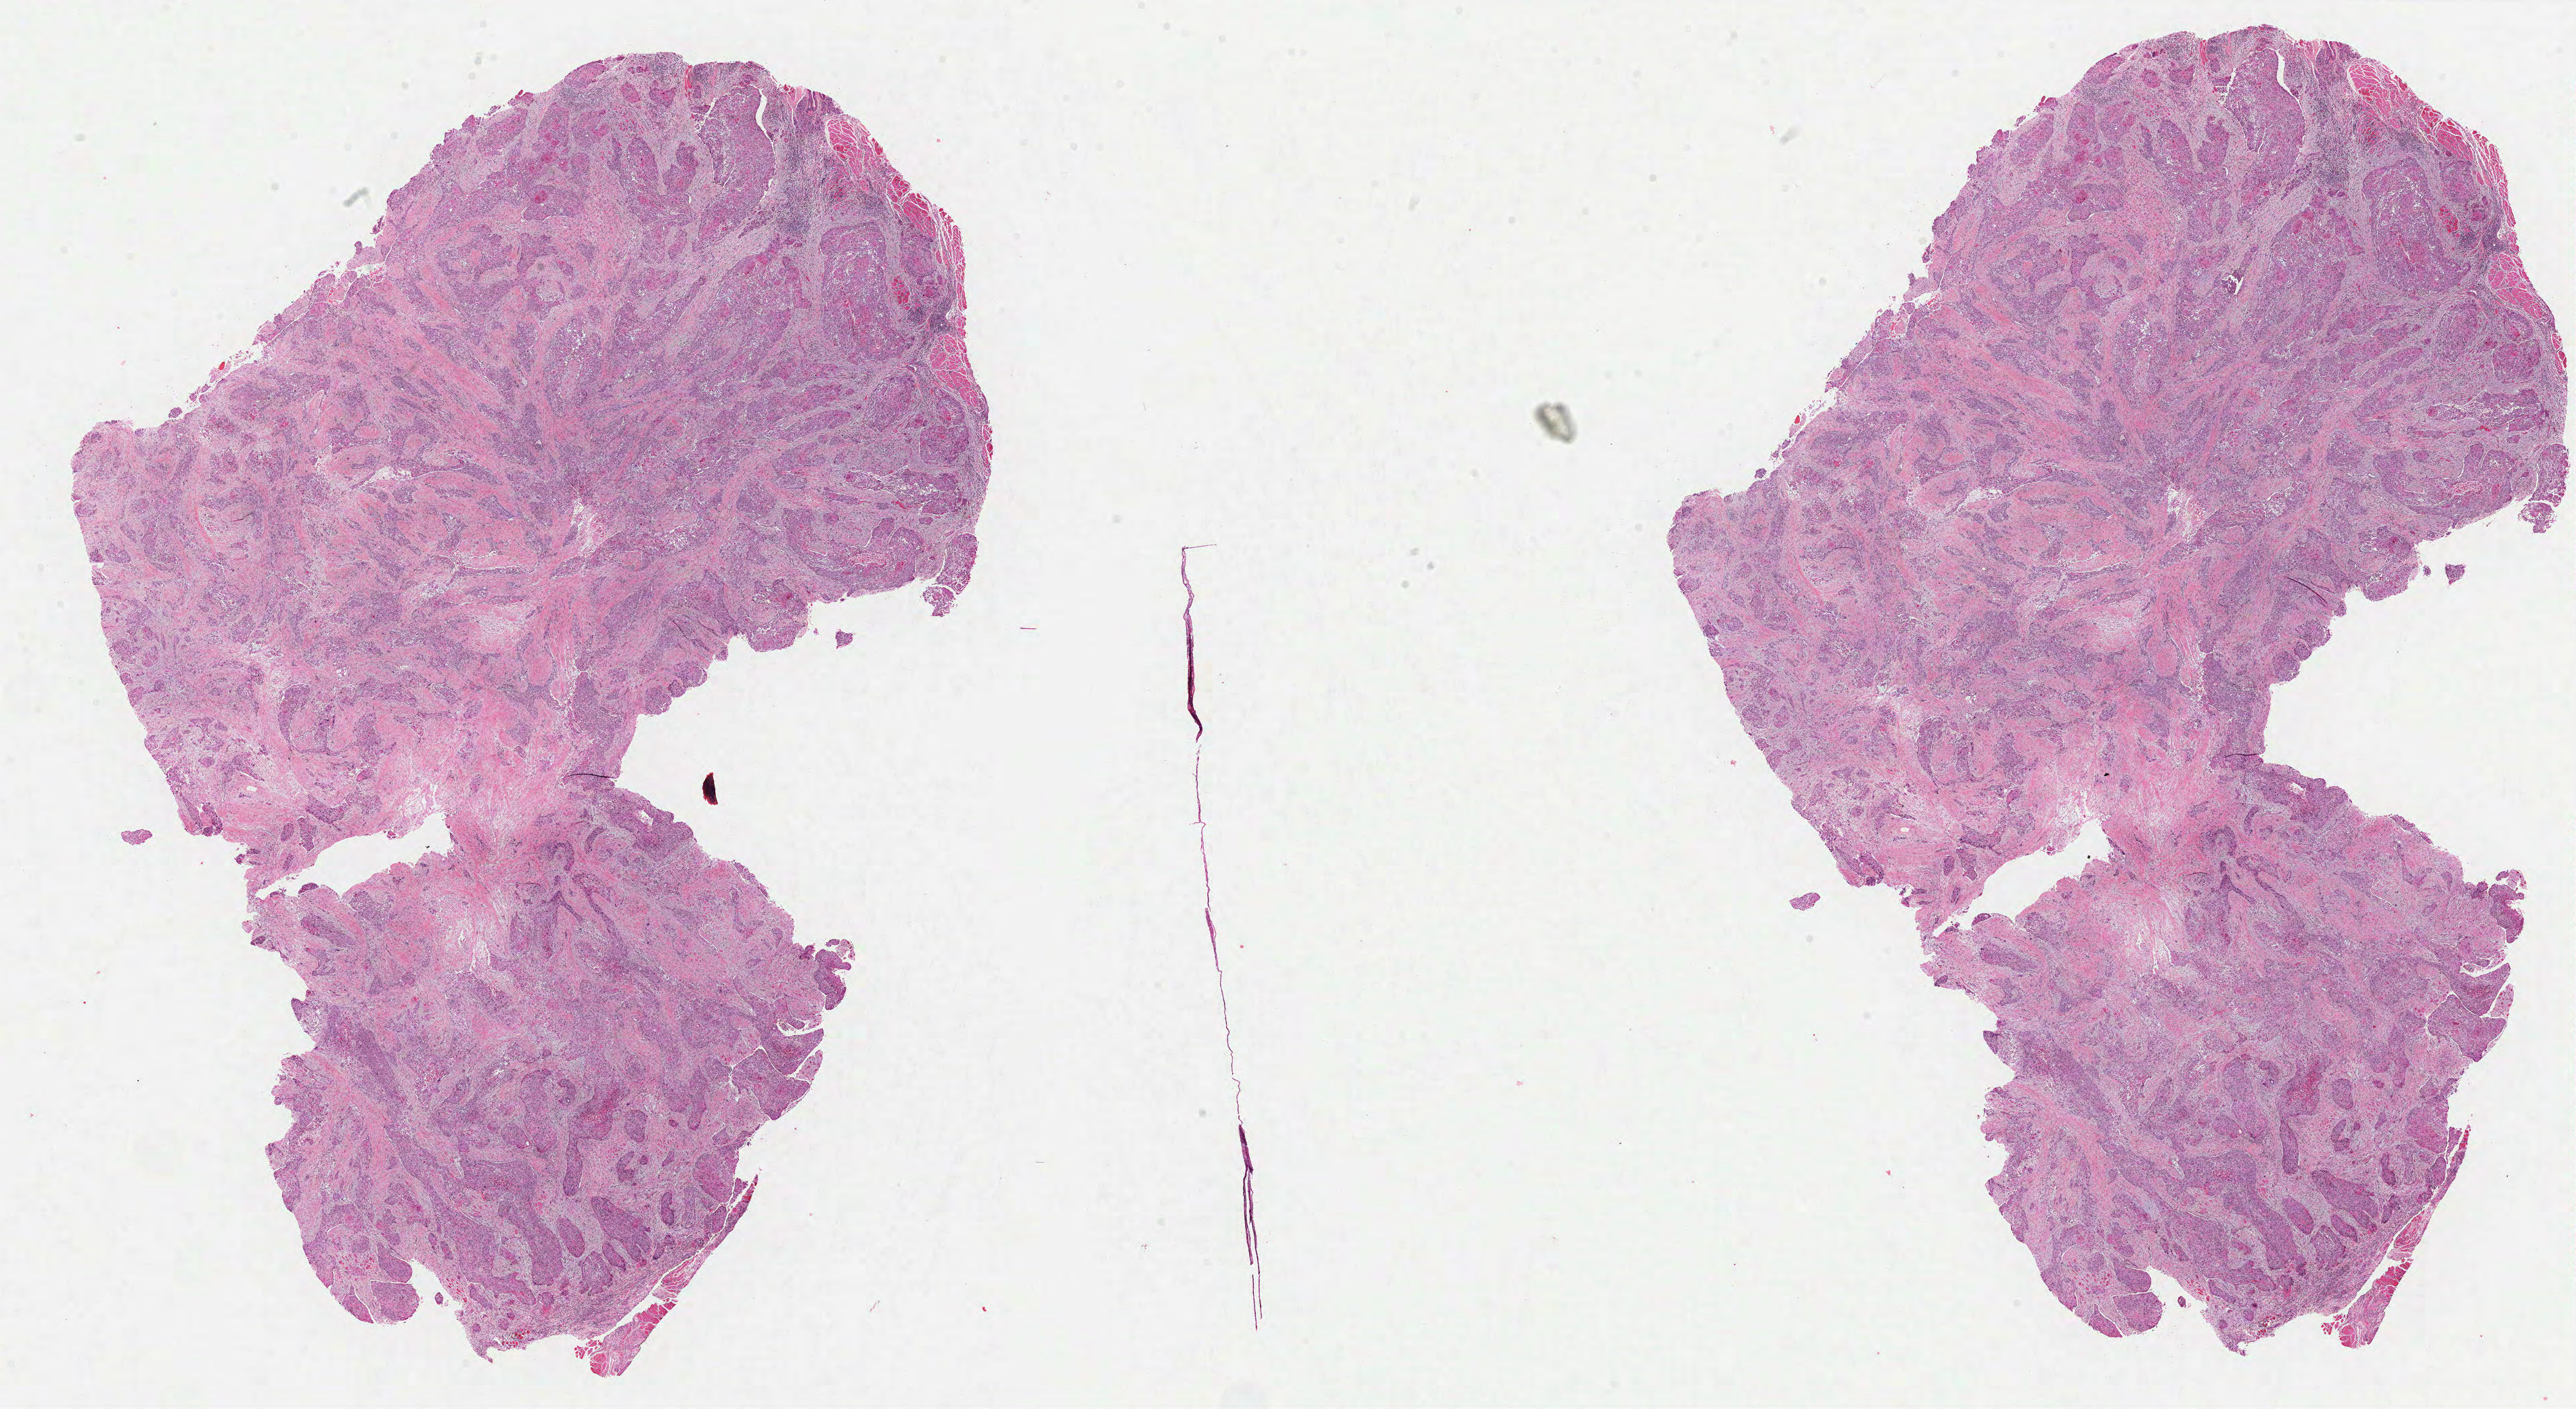
H&E-stained whole-slide image, whole scanned area (about 30.1 x 16.5 mm) shown as a low-resolution overview. Formalin-fixed paraffin-embedded (FFPE) diagnostic section. Primary tumour sample from the head and neck. Male patient; age at initial diagnosis 61 years. Histologic grade: G1 (well differentiated).
Diagnosis: Squamous cell carcinoma, NOS (tongue, NOS). Lymph nodes positive (case pathology): 1 of 17 examined. AJCC pathologic stage: III.